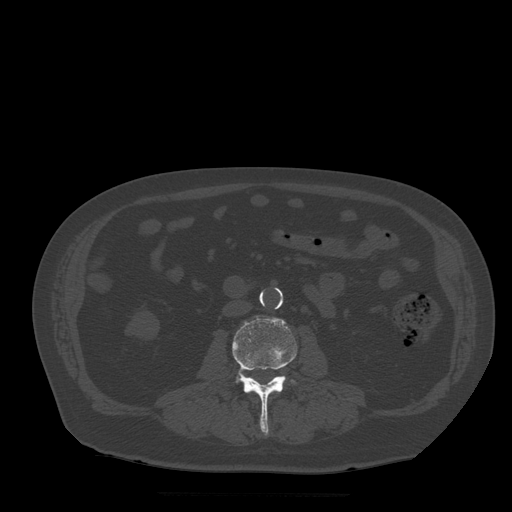
CT including the spine, one axial slice. Position 140 of 522 along the scan axis. Bone window (W 1800 / L 400 HU). 1.25 mm slice thickness. 512 × 512 image matrix, field of view 420 × 420 mm. Patient age 72 years. Case-level facts recorded for this patient, not image findings: primary cancer: prostate.
Structures marked on this image (semi-automatically segmented with operator editing):
- L3 vertebra: bounding box <233,318,297,434> (left, top, right, bottom; pixels)